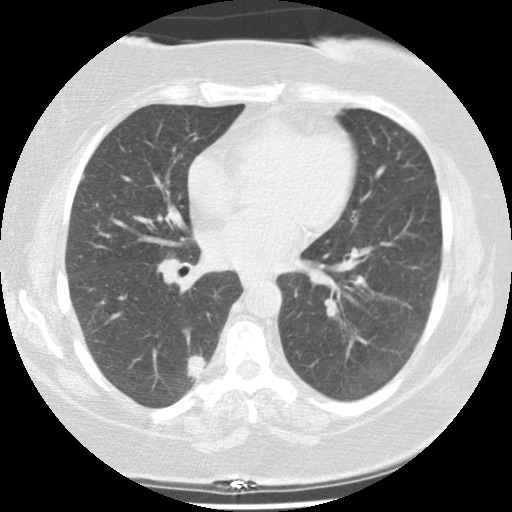
Low-dose screening chest CT, one axial slice; position 74 of 131 along the scan axis; 140 kVp; lung window (W 1500 / L -600 HU); 512 × 512 image matrix.
Structures marked on this image (expert manual segmentation):
- lesion 1 (tumor, lower lobe of right lung): bounding box <187,352,206,381> (left, top, right, bottom; pixels)